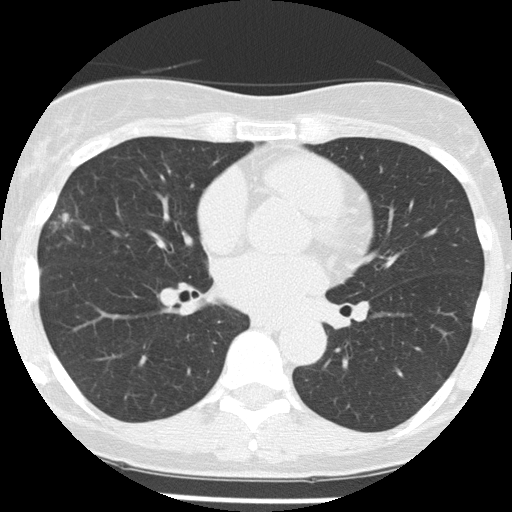
Low-dose screening chest CT, one axial slice. Slice 80 of 156 in the series (ordered by position). 120 kVp. Lung window (W 1500 / L -600 HU). 2 mm slice thickness. 512 × 512 image matrix, field of view 280 × 280 mm.
Outlined on this slice (expert manual segmentation):
- lesion 1 (tumor, middle lobe of right lung): box from (x=59, y=213) to (x=69, y=223) px